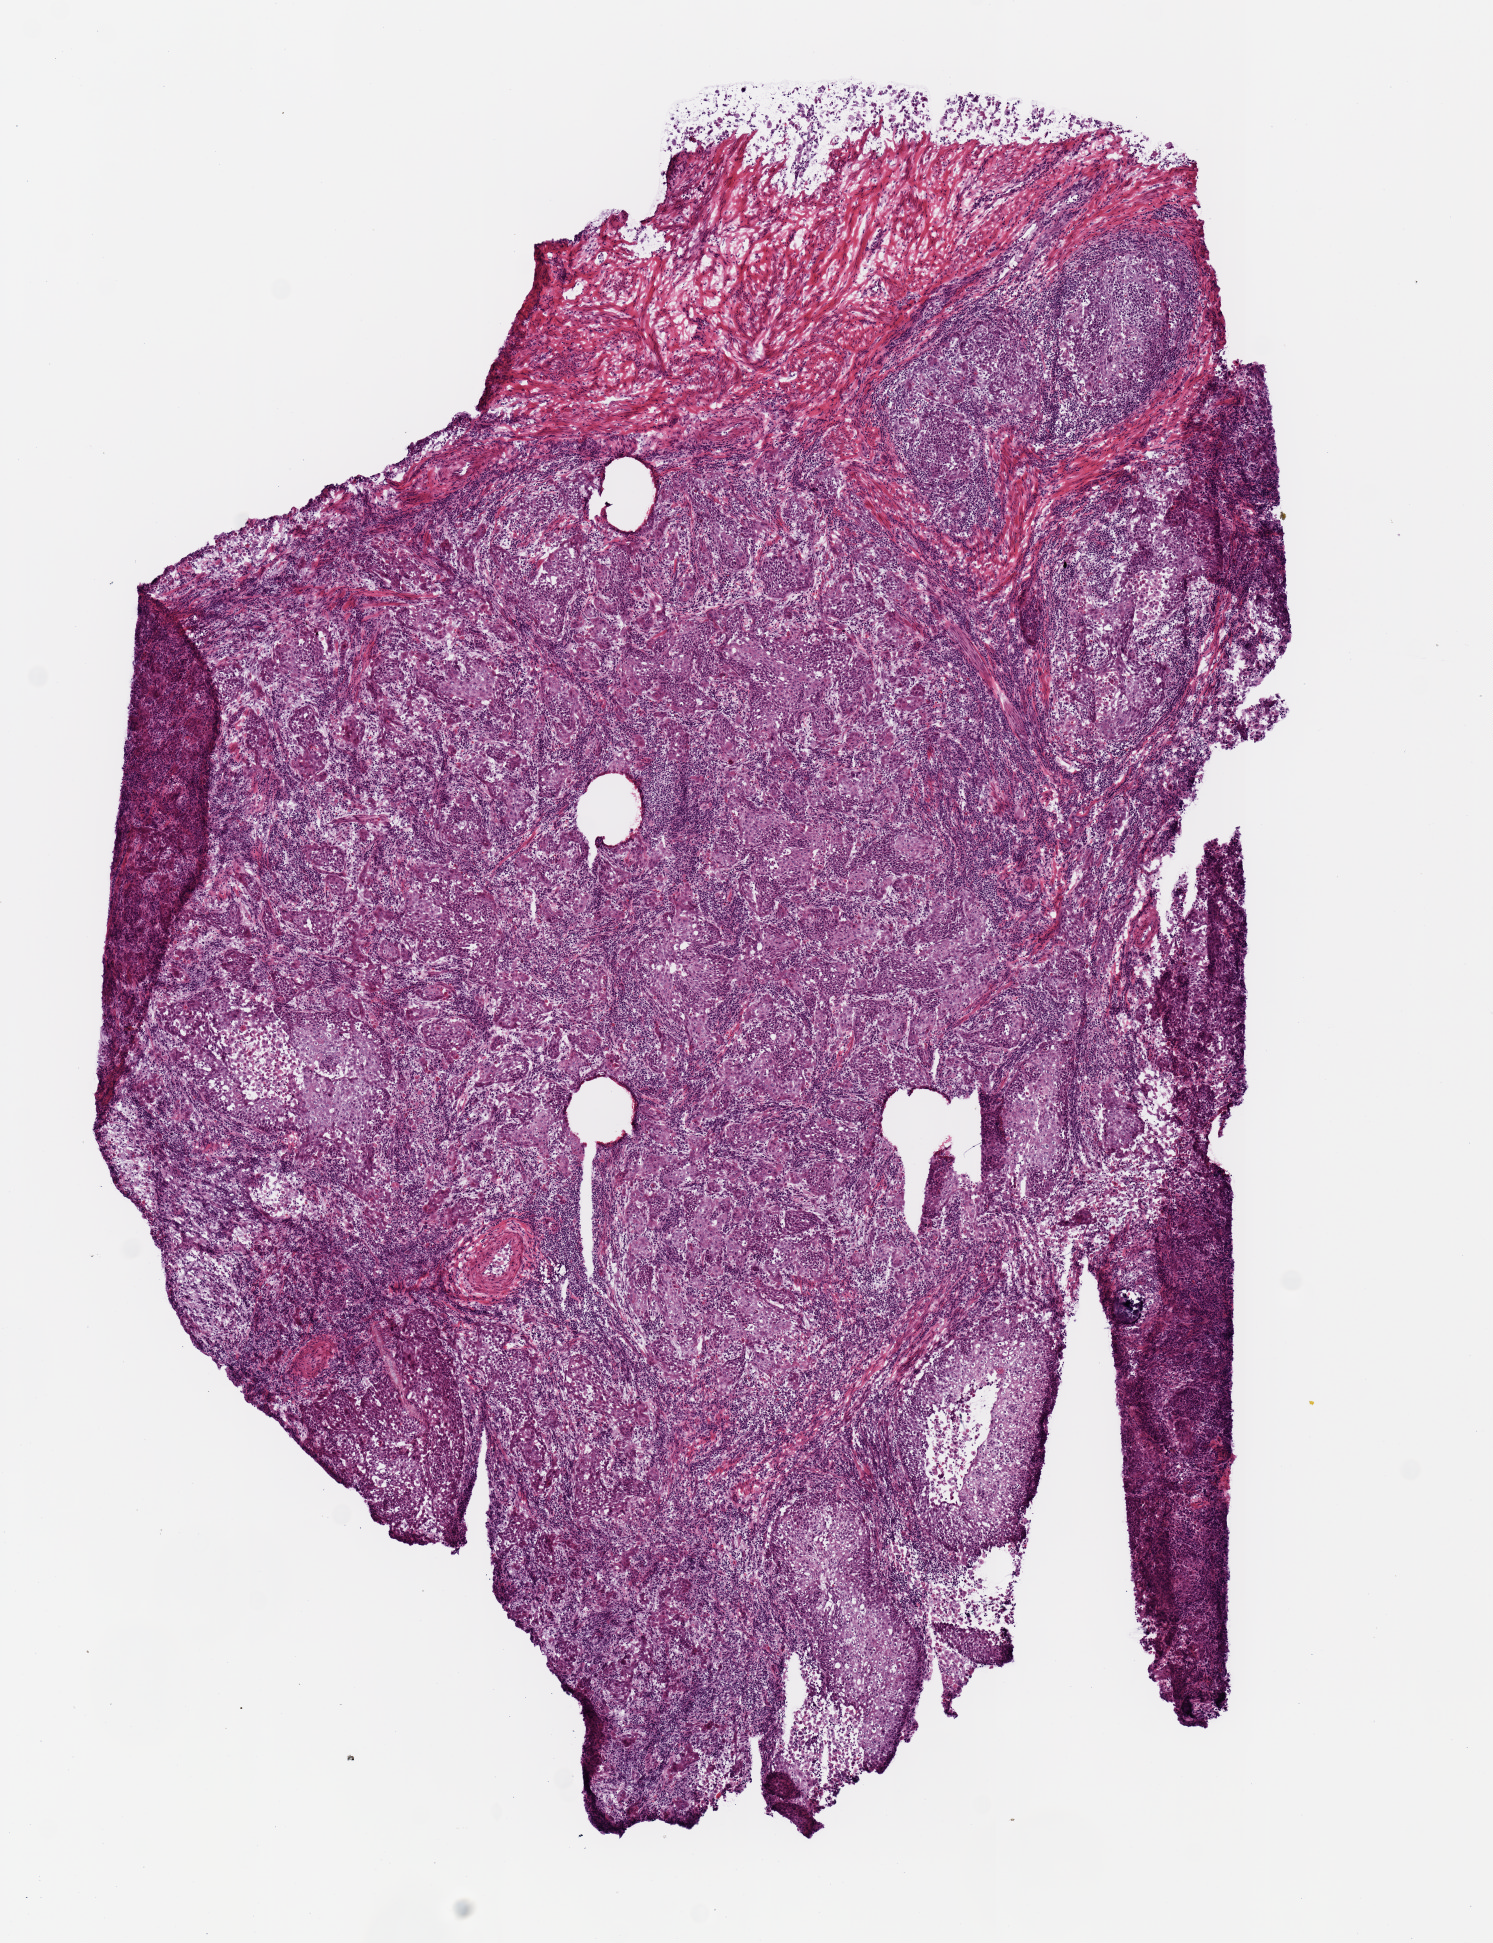
Whole-slide histology image, H&E — shown as a low-resolution overview of the whole scanned area (about 5.9 x 7.7 mm); frozen section from the top of the tissue portion; cervix, primary tumour sample. Female, age 35 years at initial diagnosis. Histologic grade: G1 (well differentiated). Composition of this section per pathologist review: tumour nuclei 60%, normal cells 92%, stromal cells 0%, necrosis 5%. Inflammatory infiltration, as recorded: lymphocyte infiltration 3%, monocyte infiltration 0%, neutrophil infiltration 0%.
FIGO stage: IB1. Pathologic diagnosis: Squamous cell carcinoma, NOS (cervix uteri). Lymph nodes positive (case pathology): 0 of 24 examined.